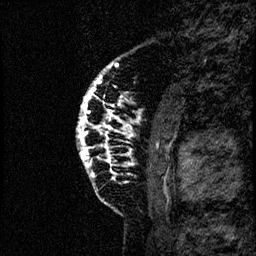
Breast MRI (dynamic contrast-enhanced), one sagittal slice. Position 15 of 60 along the scan axis. Dynamic contrast-enhanced study with each time point stored as its own series, time point 2 of 4 at this slice position (early post-contrast, ordered by acquisition time). 1.5 T. TE 4.2 ms, TR 17.6 ms. 256 × 256 image matrix, field of view 200 × 200 mm. Patient: female, 40 years. From the clinical record (not read from this slice): setting: breast cancer imaged before/during neoadjuvant chemotherapy; receptor status: HER2-positive.
Structures marked on this image (semi-automatically segmented with operator editing):
- analysis volume of interest (the breast-tissue region the enhancement analysis was run in; not a lesion): box from (x=73, y=55) to (x=185, y=206) px
- tumour enhancement mask (voxels above the 100 % enhancement threshold inside the analysis volume of interest): (x=77, y=62)–(x=158, y=168)